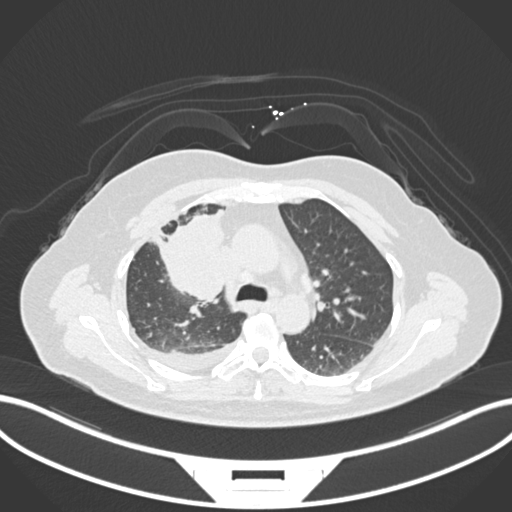
Chest CT, one axial slice; position 103 of 172 along the scan axis; reconstruction kernel B30f; lung window (W 1500 / L -600 HU); 1 mm slice thickness; 512 × 512 image matrix, field of view 400 × 400 mm. Female patient, age 52 years. Case-level facts recorded for this patient, not image findings: clinical TNM (as recorded): T3 N1 M1.
Outlined on this slice (rectangle marked by the reading radiologist):
- lung tumour (recorded histology: adenocarcinoma): bounding box <149,207,228,303> (left, top, right, bottom; pixels)